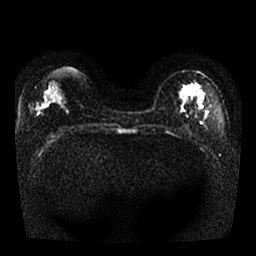
Breast MRI, one axial slice. Slice 14 of 25 in the series (ordered by position). Diffusion-weighted series; image 2 of 4 stored at this slice position (different b-values; order by instance number). 1.5 T. 4 mm slice thickness. 256 × 256 image matrix, field of view 330 × 330 mm. Female patient.
Structures marked on this image (manually delineated by an expert):
- tumour on diffusion-weighted imaging: bounding box <195,86,202,90> (left, top, right, bottom; pixels)